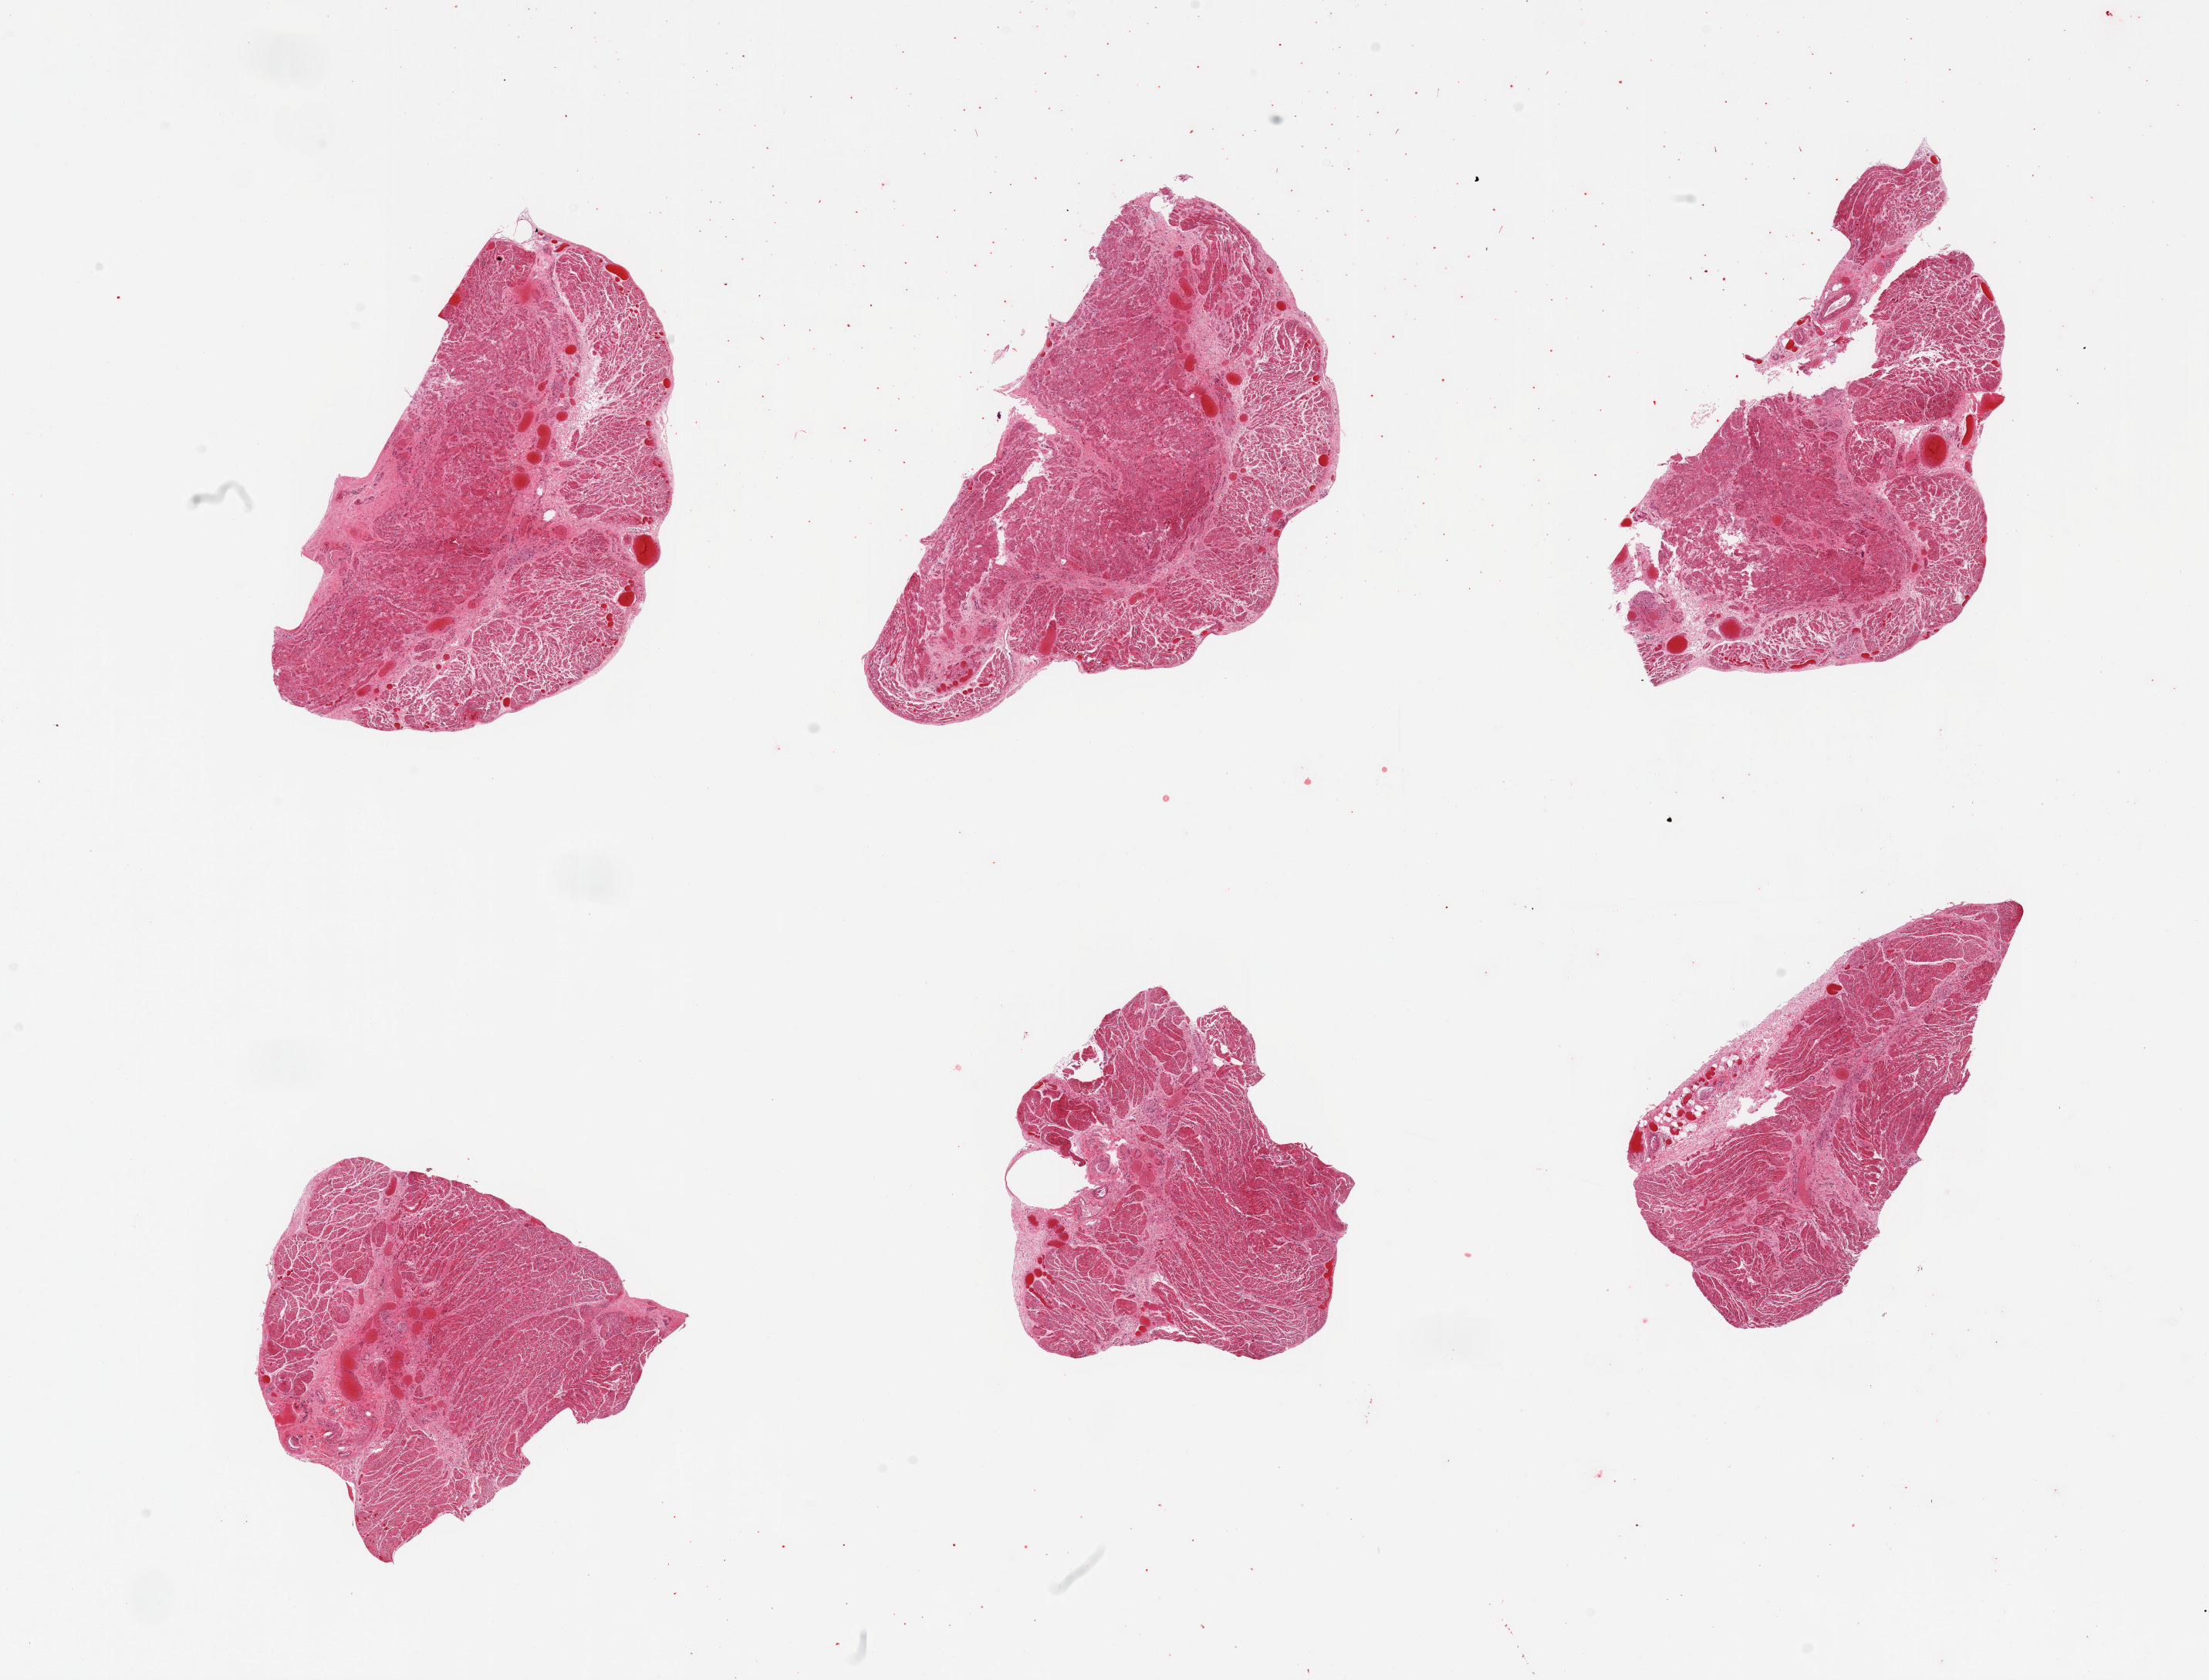
Whole-slide image, H&E stain, brightfield — low-resolution overview of the scanned area, about 22.6 x 17.2 mm (acquisition: 20x scan), PAXgene-fixed paraffin-embedded (PFPE) section, sampled site (target tissue): gastroesophageal junction, donor tissue sample. Donor: female.
* reviewer comment on this tissue sample: 6 pieces; well trimmed muscularis